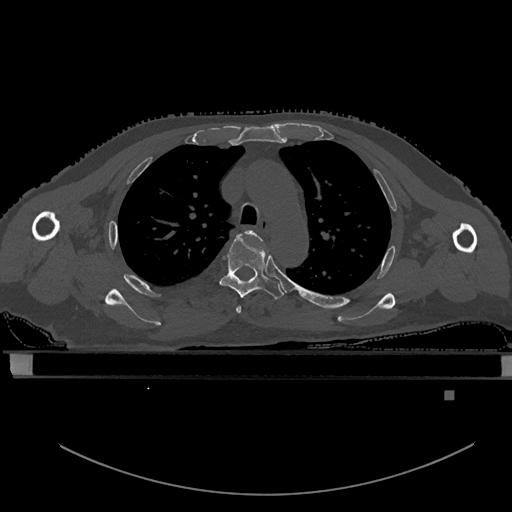
CT including the spine, one axial slice; position 411 of 969 along the scan axis; bone window (W 1800 / L 400 HU); 0.5 mm slice thickness; 512 × 512 image matrix. Patient: male, 82 years. From the clinical record (not read from this slice): primary cancer: prostate; vertebrae with lytic lesions (as recorded): T11, T9, T8, T2.
Outlined on this slice (semi-automatically segmented with operator editing):
- T3 vertebra: bounding box (x1, y1, x2, y2) in pixels: (236, 230, 260, 314)
- T4 vertebra: (220, 236, 284, 299)